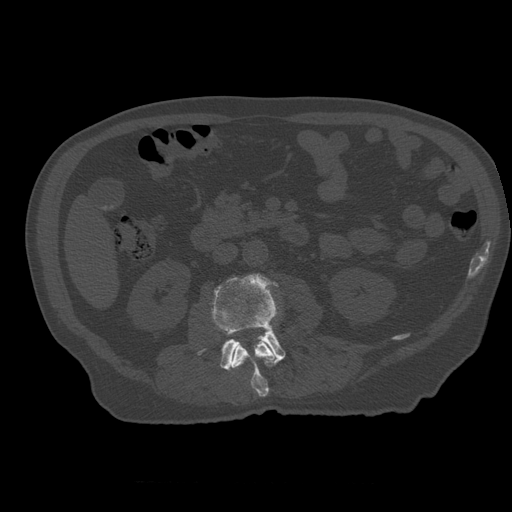
CT including the spine, one axial slice. Reconstruction kernel STANDARD. 120 kVp. Bone window (W 1800 / L 400 HU). 1.25 mm slice thickness. 512 × 512 image matrix, field of view 407 × 407 mm. Patient age 73 years. Case-level facts recorded for this patient, not image findings: primary cancer: prostate; vertebrae with lytic lesions (as recorded): L2.
Outlined on this slice (semi-automatically segmented with operator editing):
- L2 vertebra: bounding box <231,341,276,397> (left, top, right, bottom; pixels)
- L3 vertebra: <199,273,286,370>